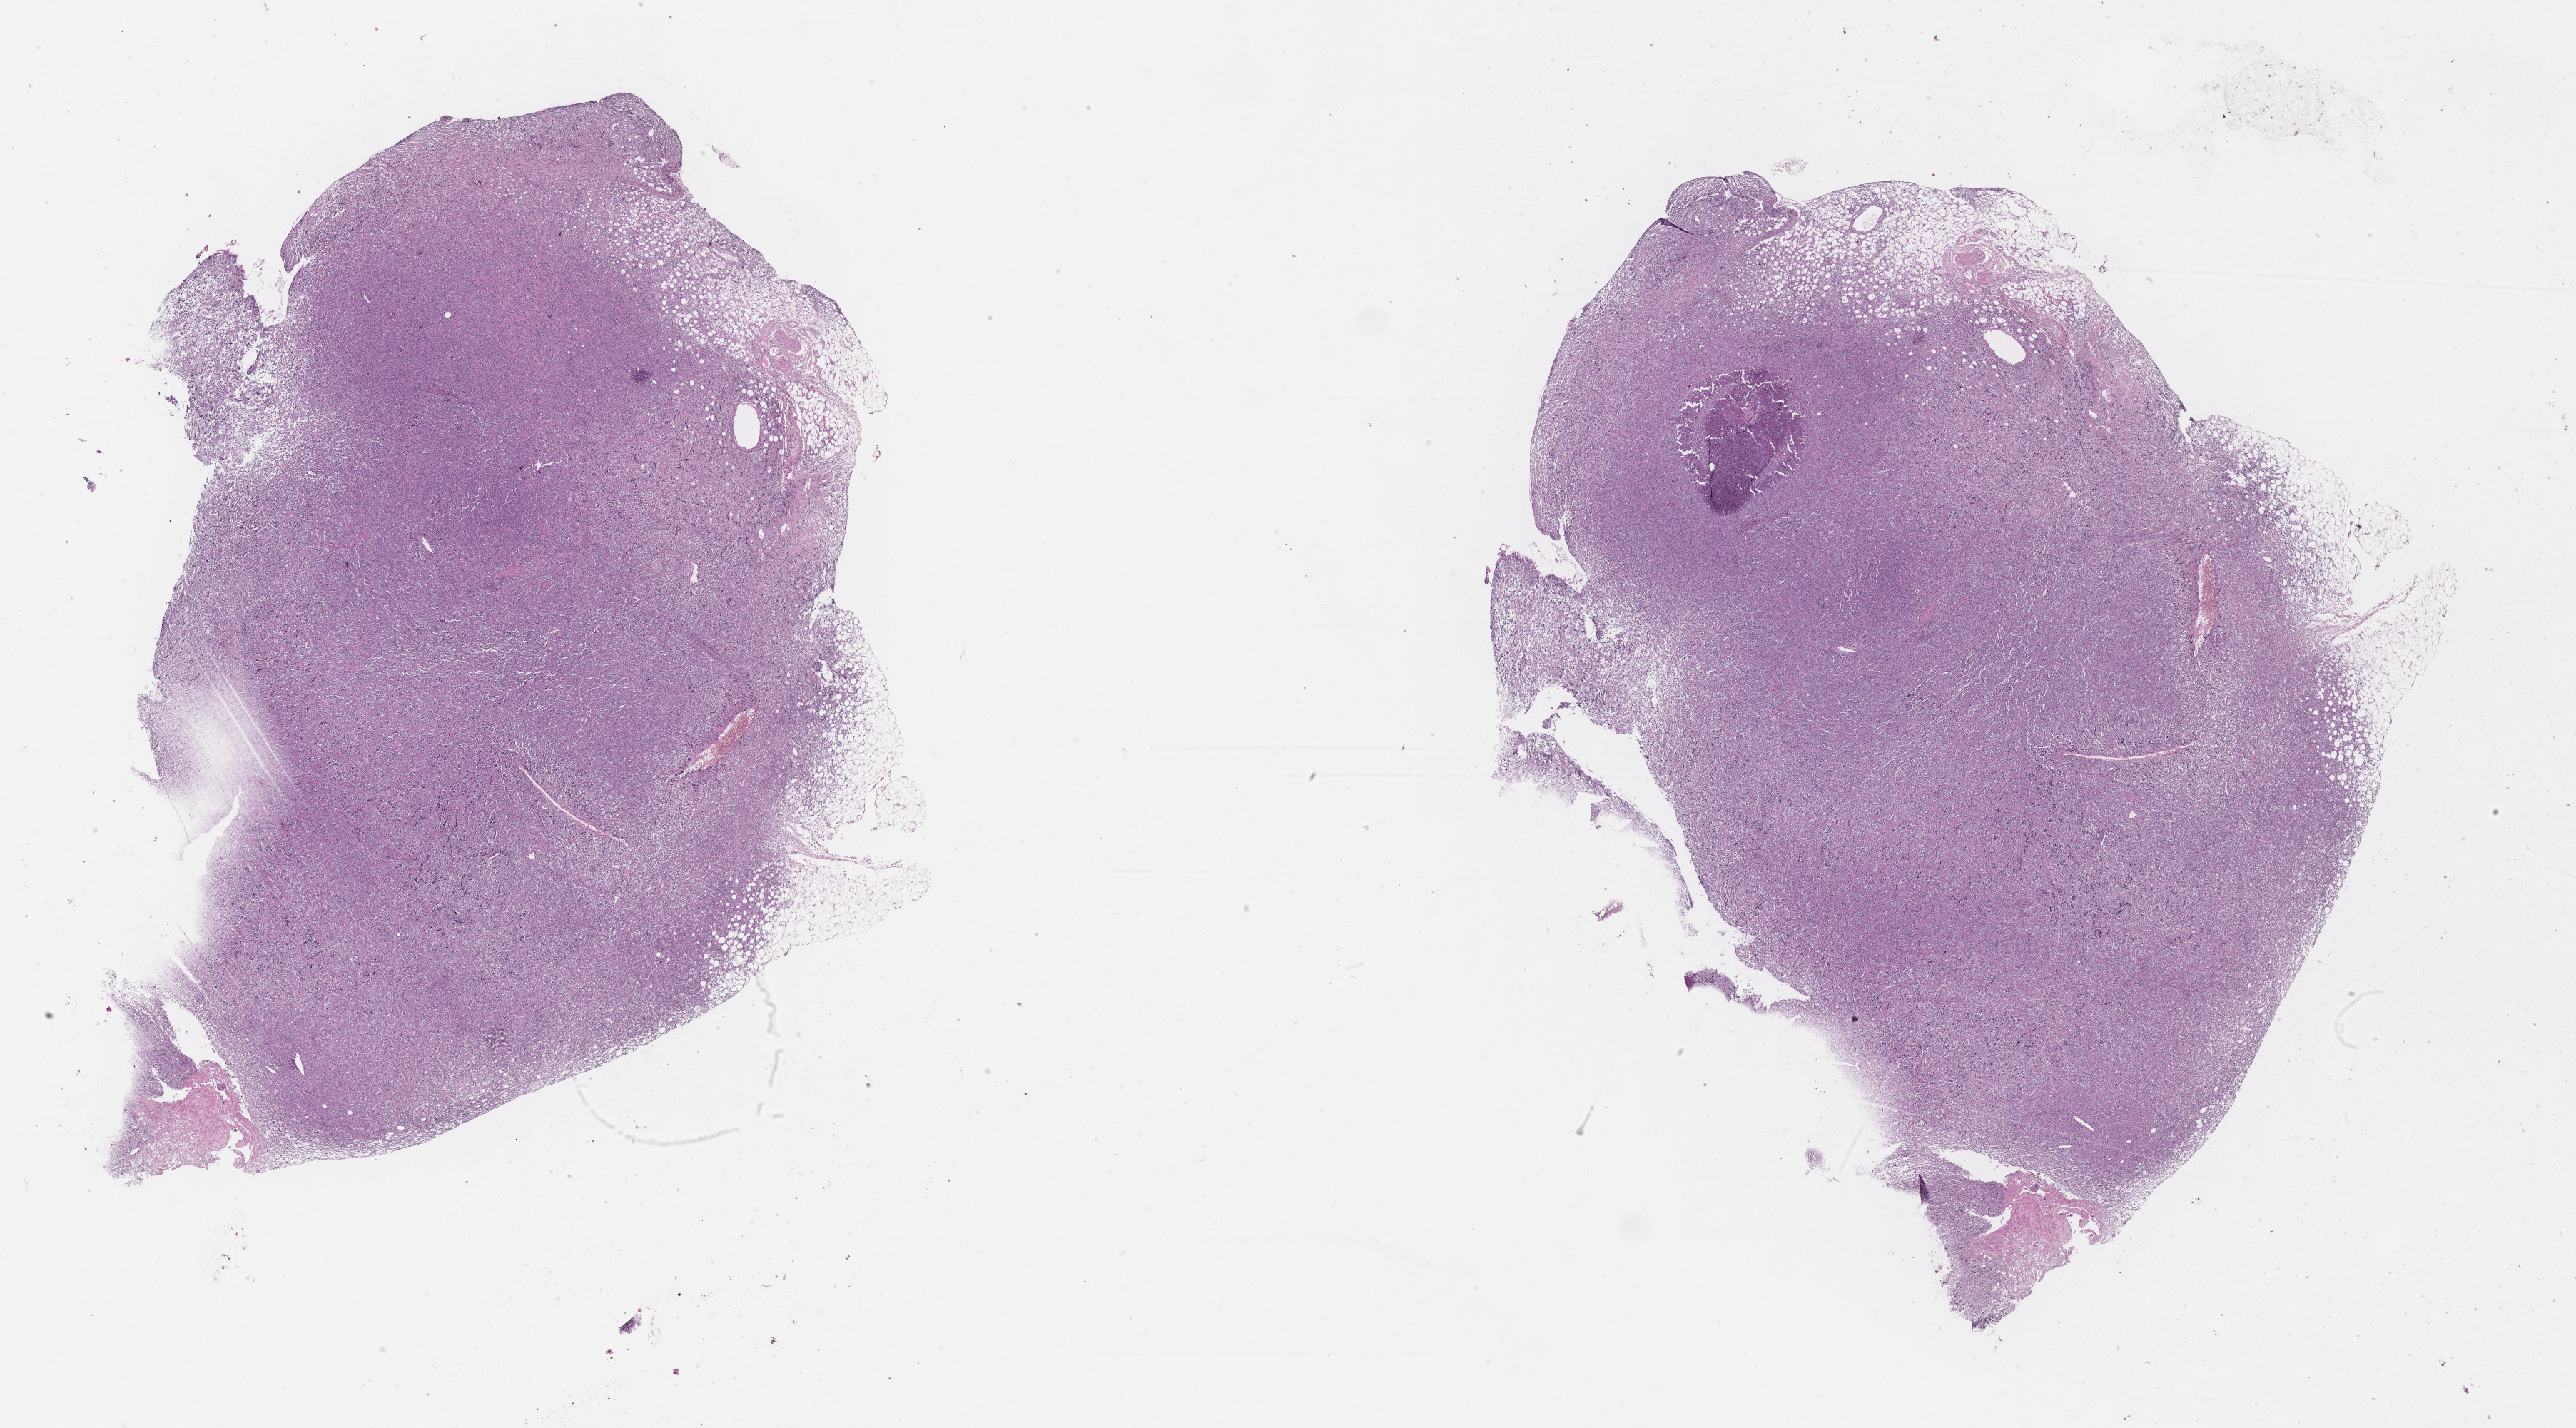
Digitized hematoxylin and eosin (H&E)-stained section, shown as a low-resolution overview of the whole scanned area (about 29.2 x 16.2 mm). Patient sex: female.
• specimen: tumor tissue